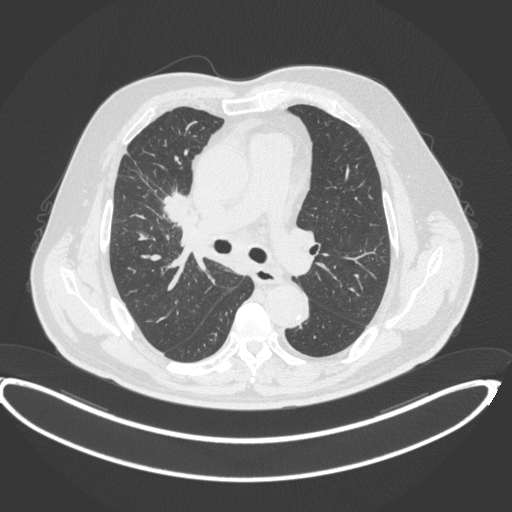
Chest CT, one axial slice; reconstruction kernel B31f; 120 kVp; lung window (W 1500 / L -600 HU); 1 mm slice thickness; 512 × 512 image matrix, field of view 448 × 448 mm. Patient: male, 62 years. From the clinical record (not read from this slice): clinical TNM (as recorded): T1c N3 M1c.
Annotated regions visible in this slice (rectangle marked by the reading radiologist):
- lung tumour (recorded histology: adenocarcinoma): bounding box (x1, y1, x2, y2) in pixels: (157, 185, 200, 232)